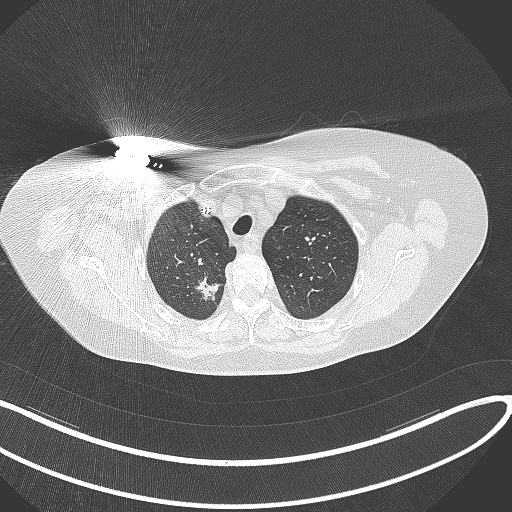
Chest CT, one axial slice; position 275 of 316 along the scan axis; reconstruction kernel B70f; 120 kVp; lung window (W 1500 / L -600 HU); 1 mm slice thickness; 512 × 512 image matrix. Patient: female, 72 years. Case-level facts recorded for this patient, not image findings: clinical TNM (as recorded): T1c N0 M0.
Outlined on this slice (rectangle marked by the reading radiologist):
- lung tumour (recorded histology: adenocarcinoma): box from (x=184, y=272) to (x=220, y=304) px